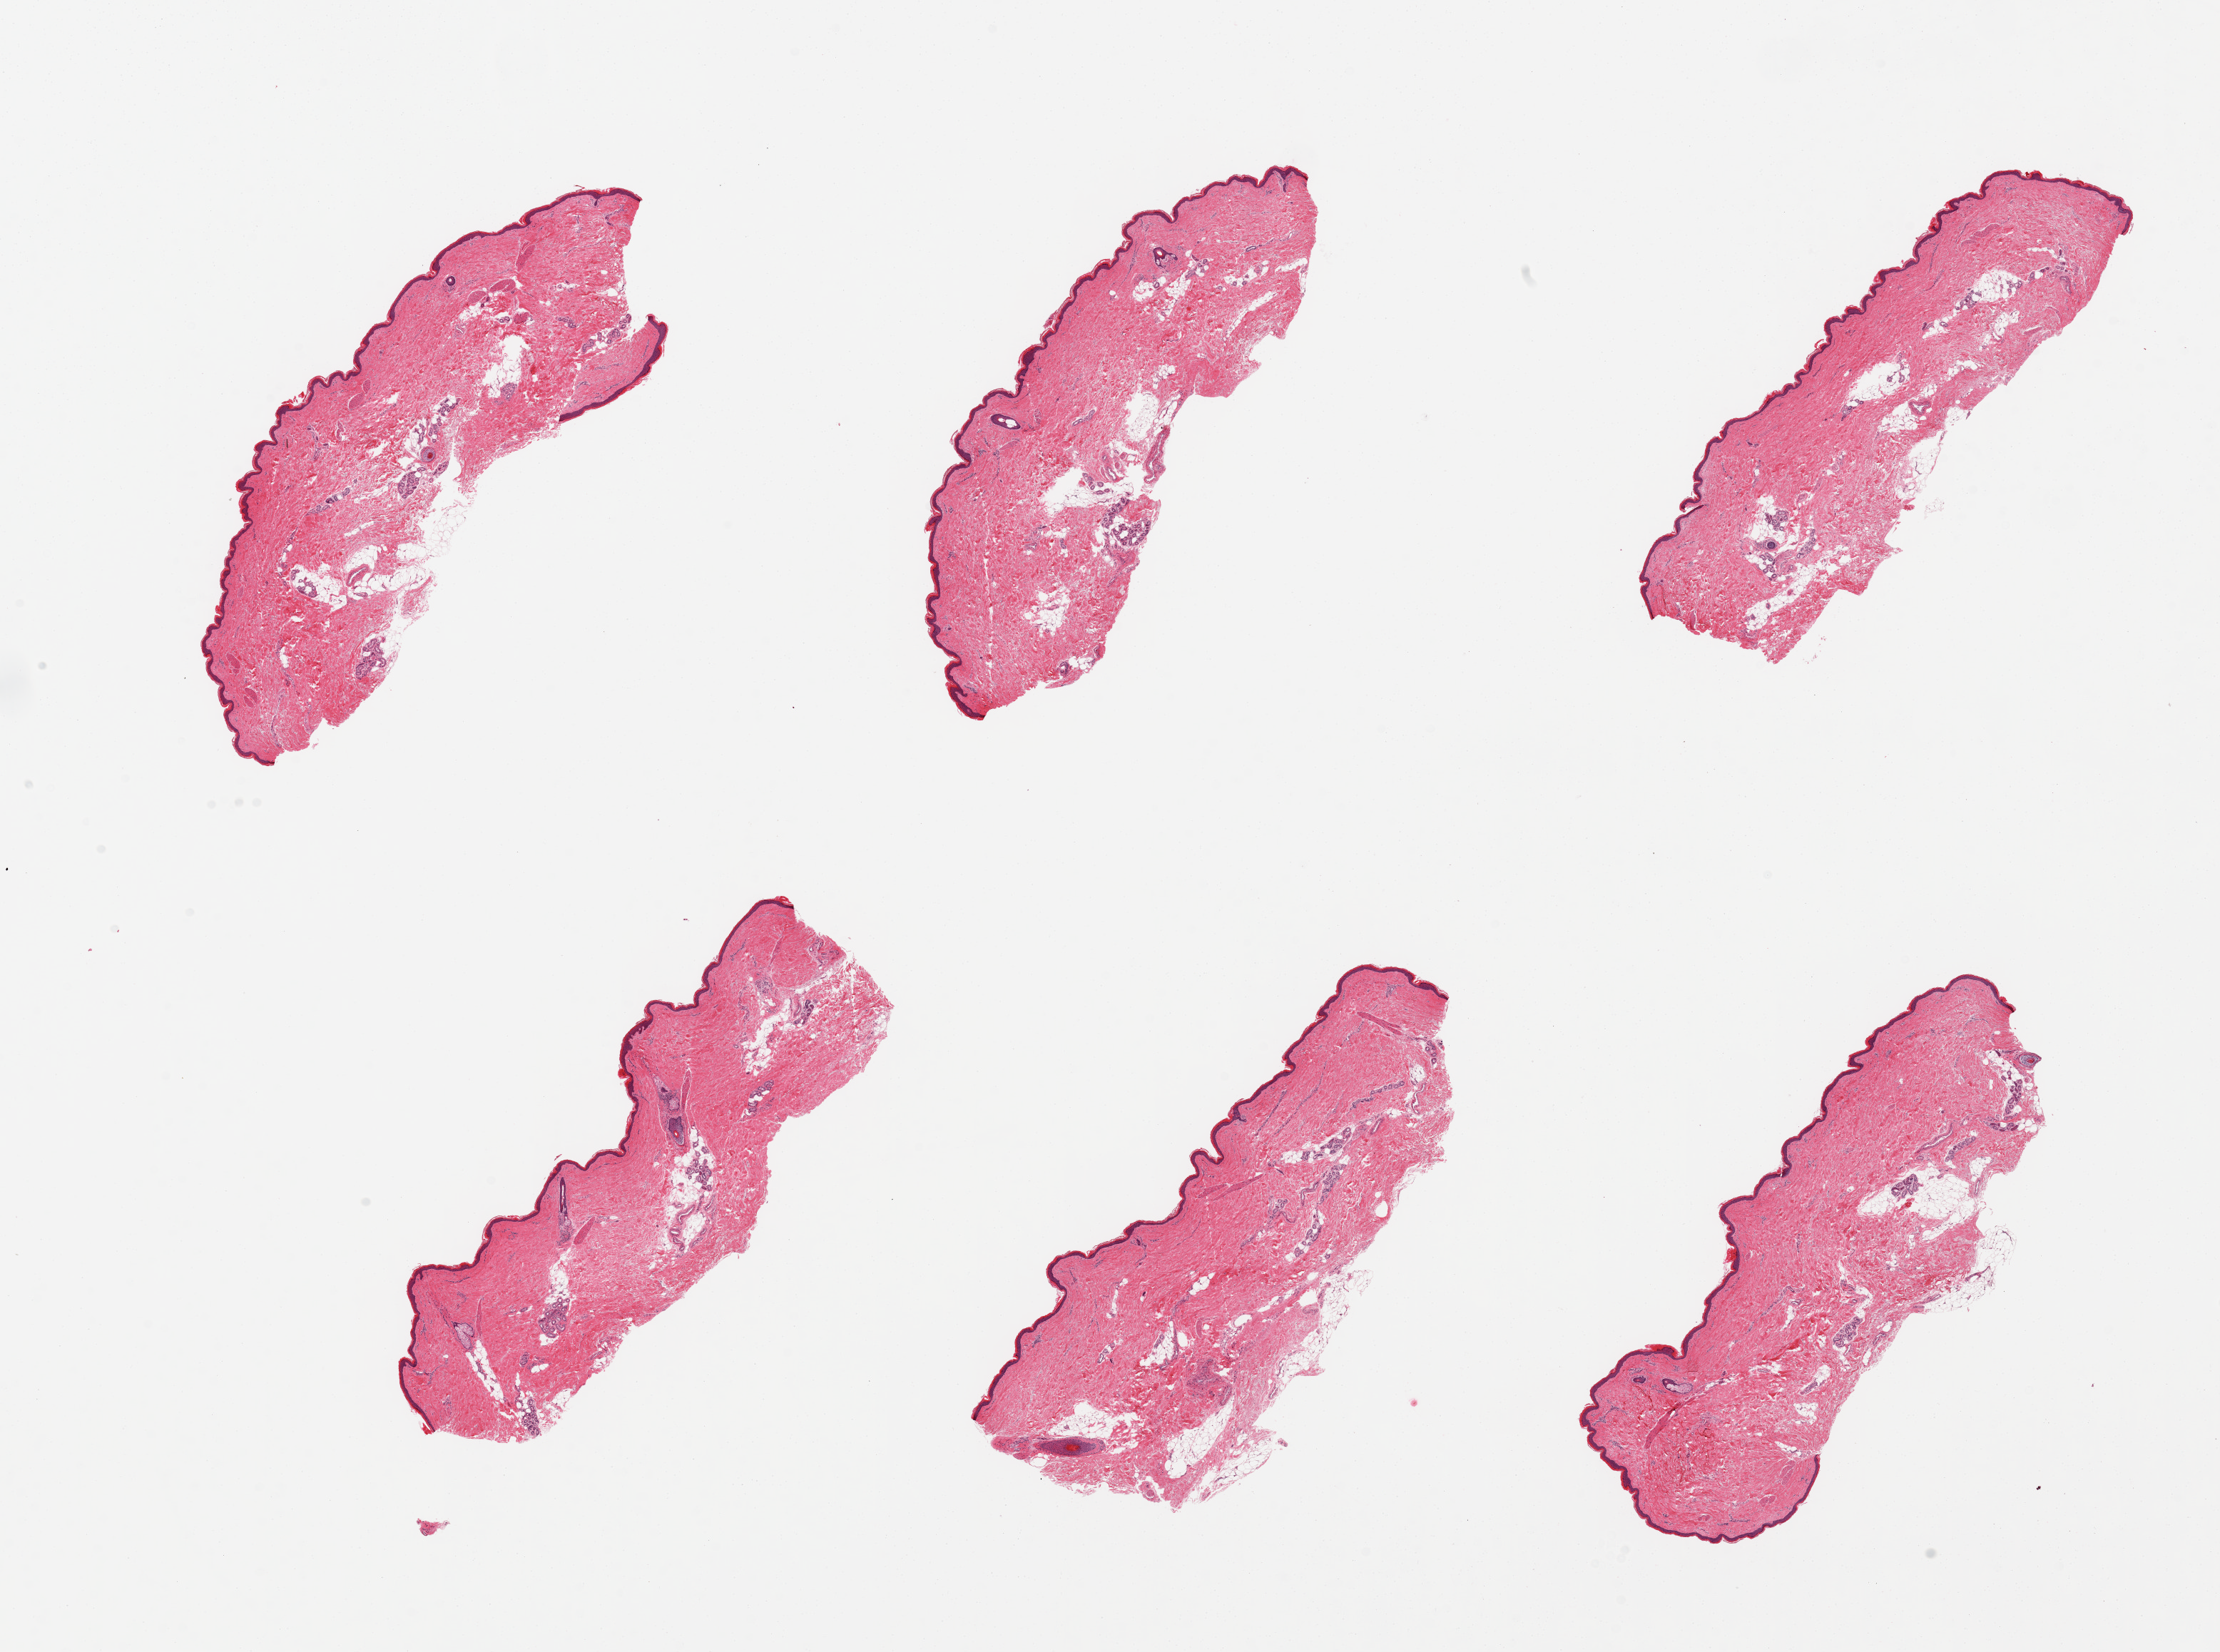
H&E whole-slide image, a low-resolution overview of the entire scanned area, about 24.6 x 18.3 mm. PAXgene-fixed, paraffin-embedded tissue. Sampled site (target tissue): skin of lower leg. Donor tissue sample. Donor: male.
• pathologist's review note for this sample: 6 pieces; well trimmed of subcutaneous fat